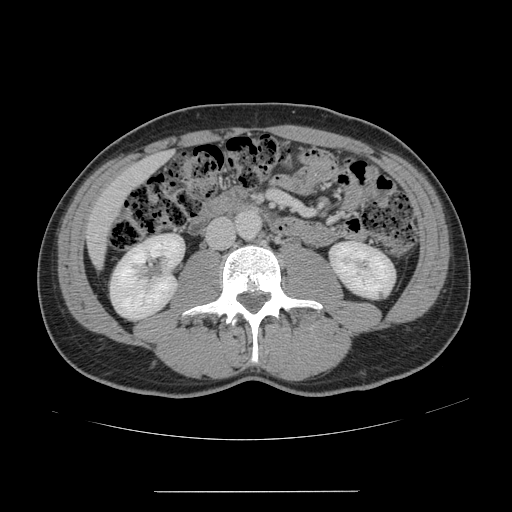
Contrast-enhanced abdominal CT, one axial slice; slice 37 of 178 in the series (ordered by position); 120 kVp; intravenous contrast given; soft-tissue window (W 400 / L 40 HU); 512 × 512 image matrix. Male patient, age 53 years. Case-level facts recorded for this patient, not image findings: diagnosis: colorectal cancer liver metastases, imaged before liver resection; multiple liver metastases: yes; largest metastasis: 2.4 cm.
Structures marked on this image (manually delineated by an expert):
- liver: box from (x=88, y=154) to (x=168, y=265) px